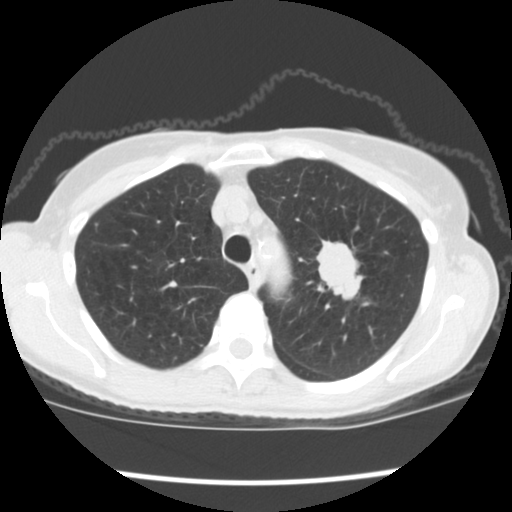
Low-dose screening chest CT, one axial slice; slice 141 of 176 in the series (ordered by position); 120 kVp; lung window (W 1500 / L -600 HU); 2.5 mm slice thickness; 512 × 512 image matrix, field of view 318 × 318 mm.
Annotated regions visible in this slice (outlined manually by an expert reader):
- lesion 1 (tumor, upper lobe of left lung): box from (x=316, y=240) to (x=366, y=305) px